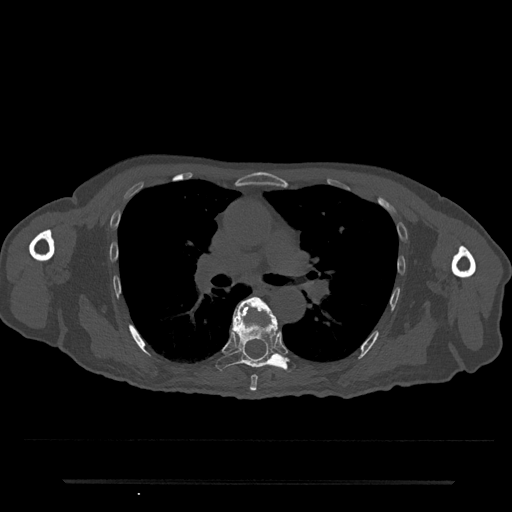
CT including the spine, one axial slice. Slice 496 of 797 in the series (ordered by position). Reconstruction kernel Br40s/3. Bone window (W 1800 / L 400 HU). 512 × 512 image matrix, field of view 427 × 427 mm. Male patient, age 74 years. From the clinical record (not read from this slice): primary cancer: prostate.
Annotated regions visible in this slice (semi-automatic segmentation, software-assisted and operator-edited):
- T6 vertebra: bounding box [x1, y1, x2, y2] px = [233, 296, 277, 391]
- T7 vertebra: [216, 305, 295, 372]